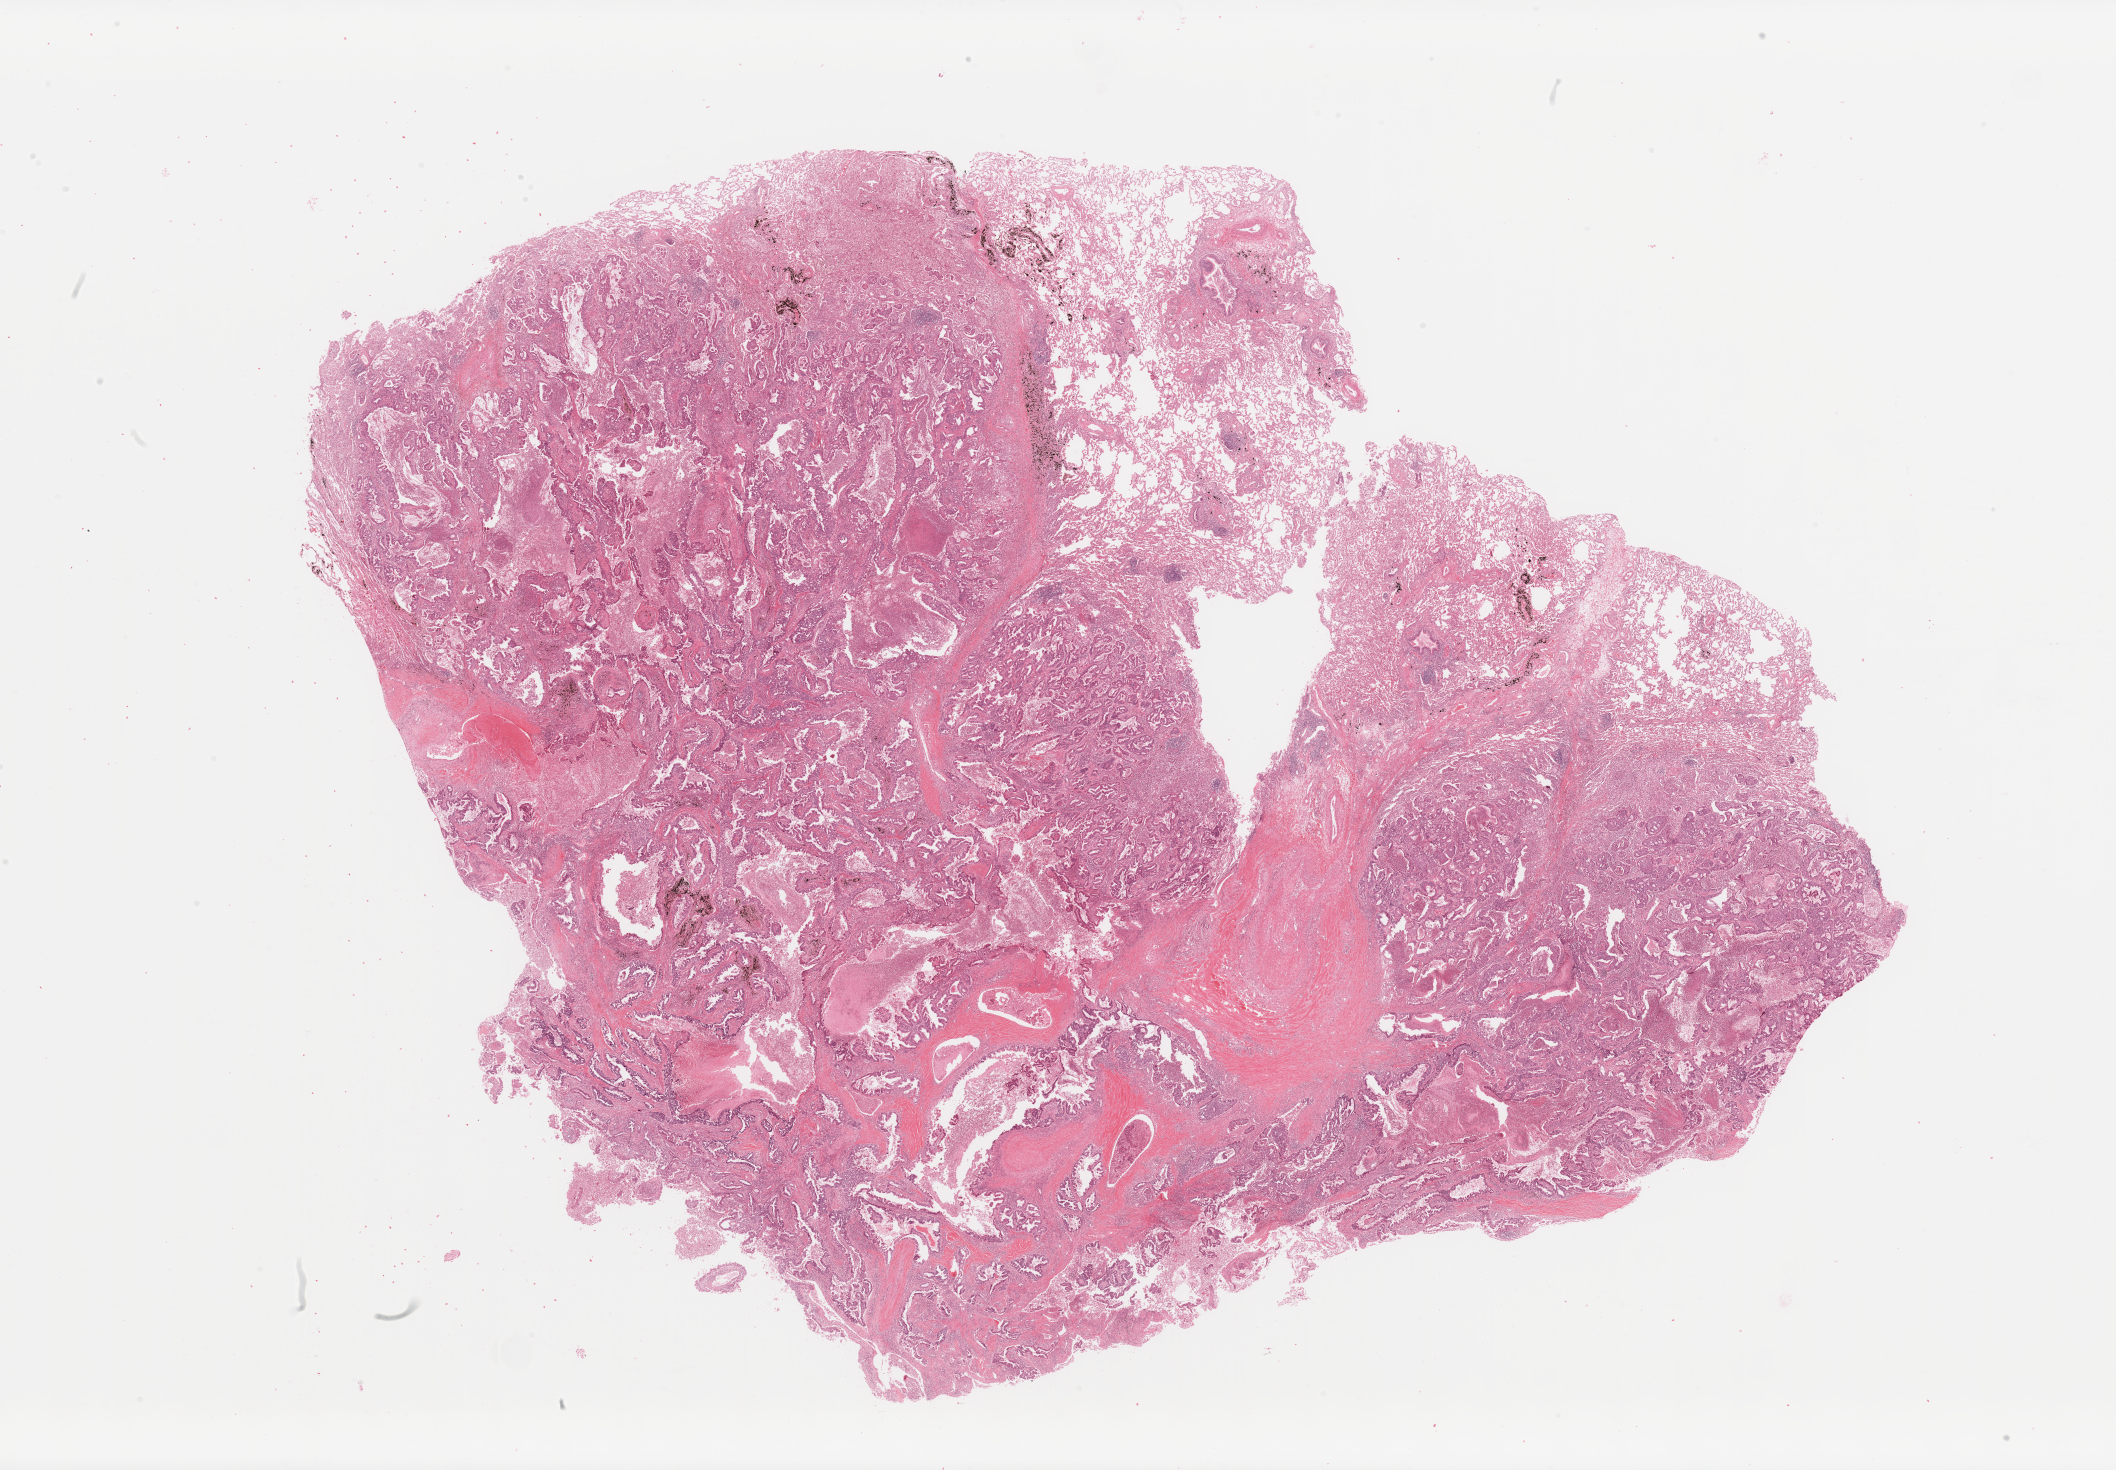
Whole-slide histology image, H&E-stained — low-resolution overview of the scanned area, about 33.5 x 23.3 mm. Lung, tumour tissue. Patient: male, age 49 years. Histologic grade: G2 (moderately differentiated).
AJCC pathologic stage: IIB. Histologic diagnosis: Adenocarcinoma, NOS.